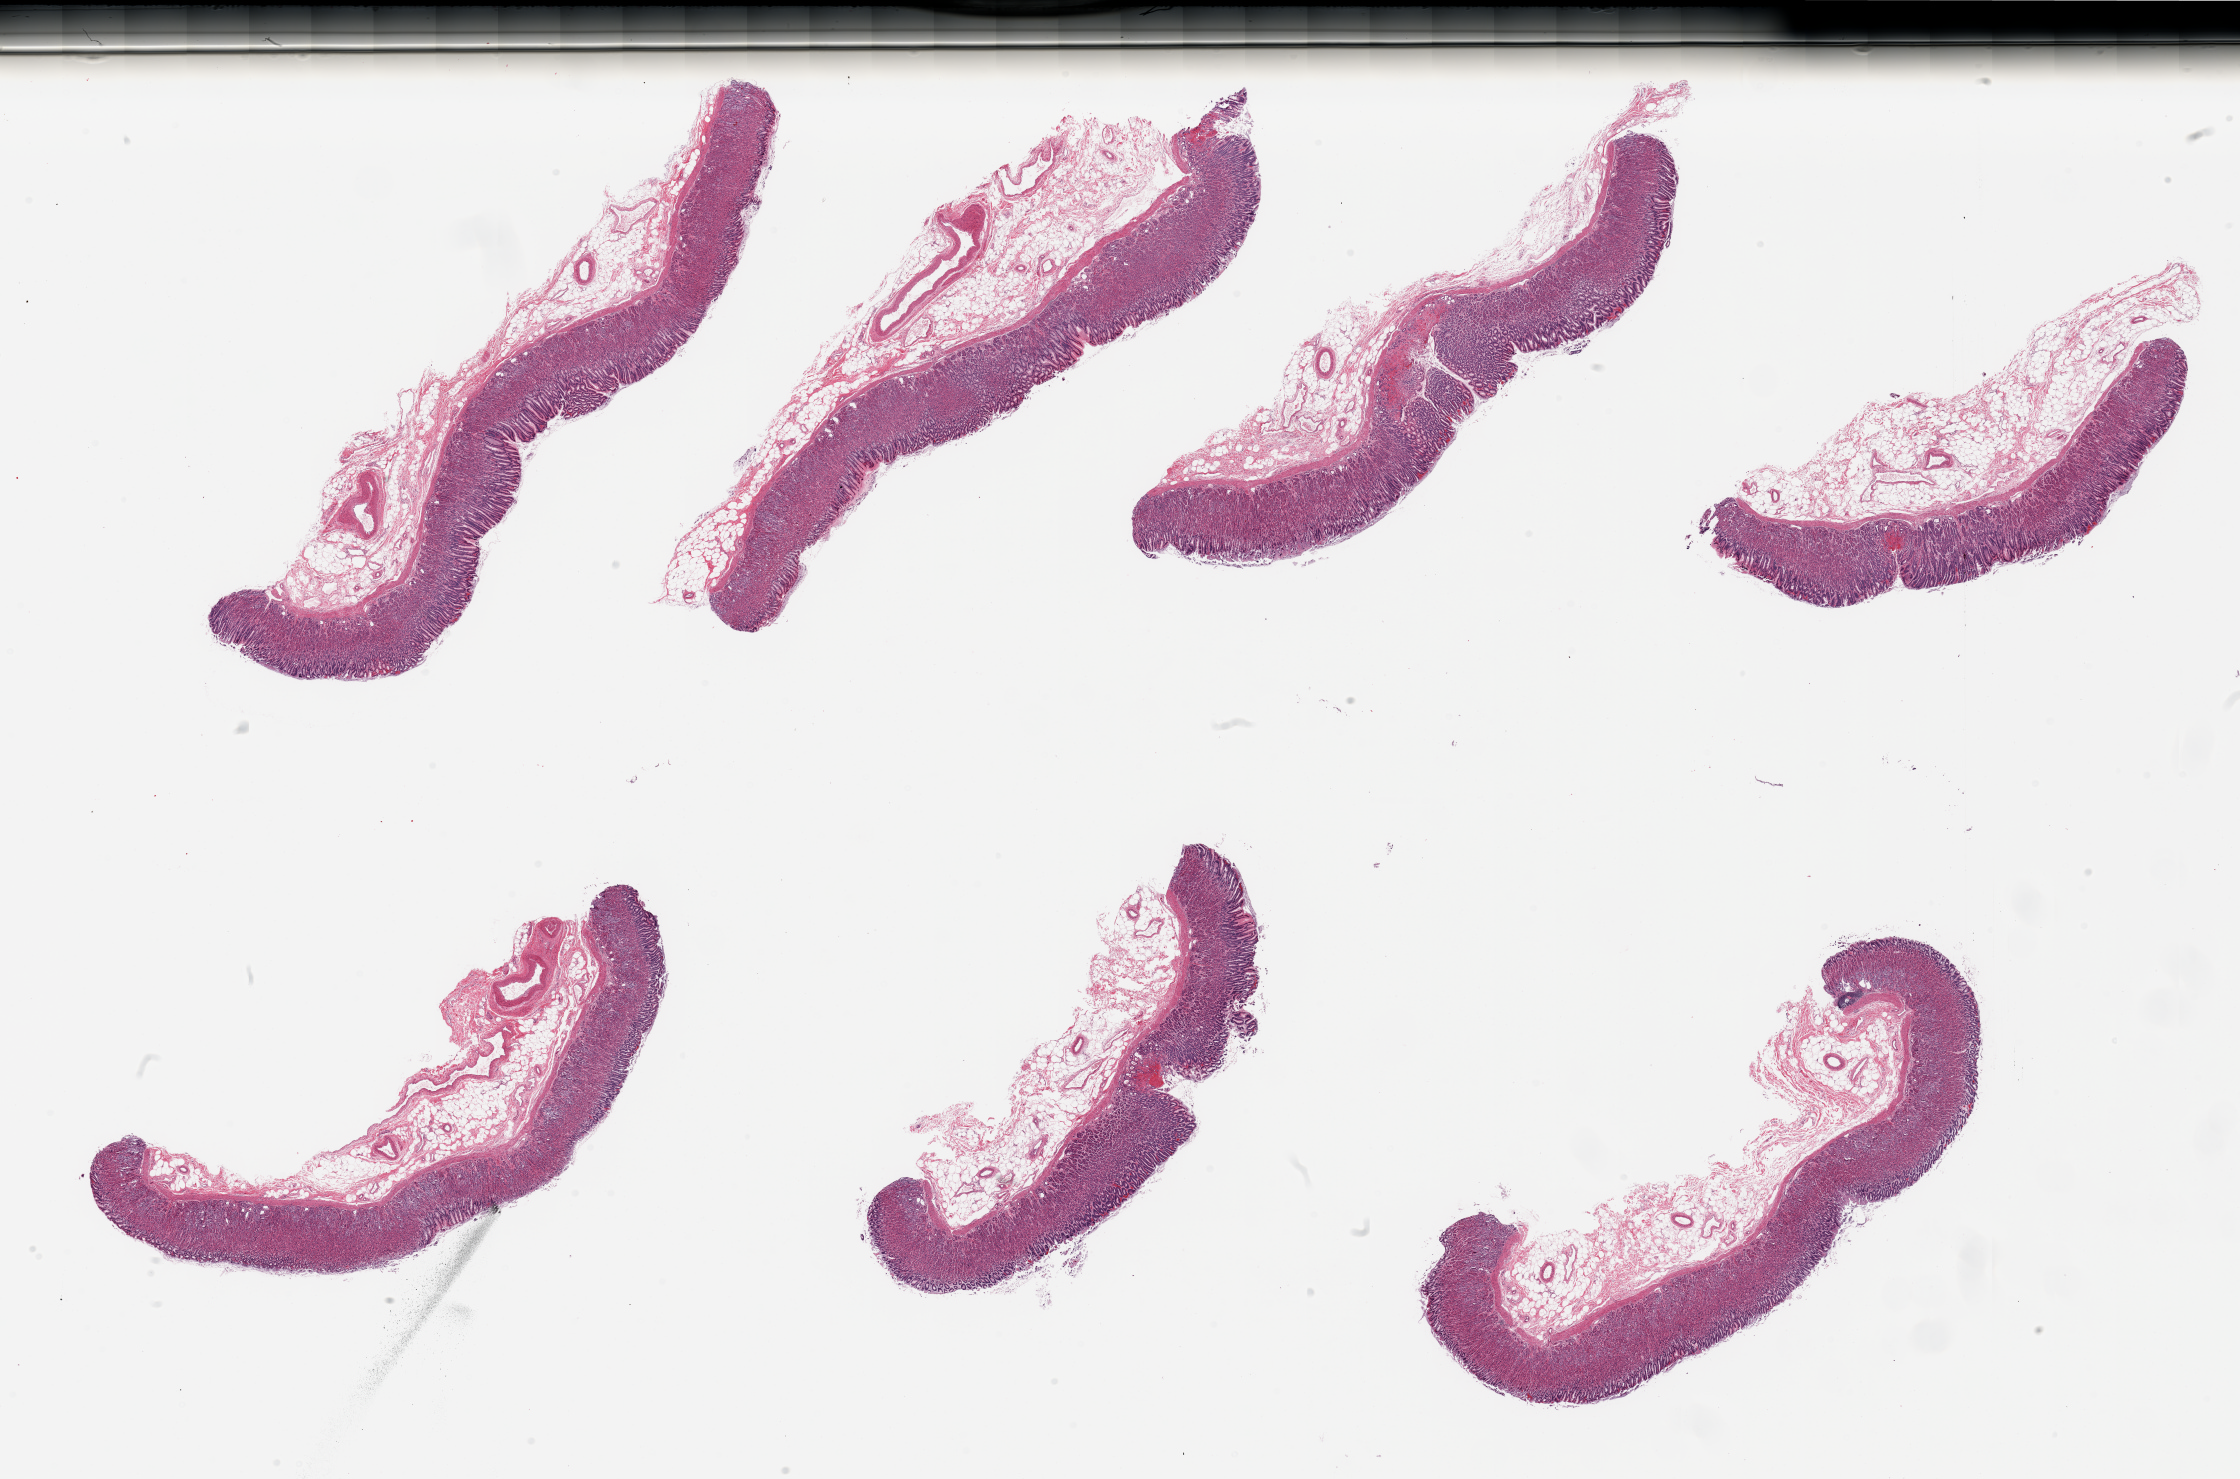
Whole-slide image, hematoxylin and eosin (H&E) stain, shown as a low-resolution overview of the whole scanned area (about 35.4 x 23.4 mm, slide scanned at 20x), PAXgene-fixed paraffin-embedded (PFPE) section, section of stomach (target tissue), donor tissue sample. Donor sex: male.
Review note (as recorded): 7 pieces; focal erosions; mucosa only, no muscularis.